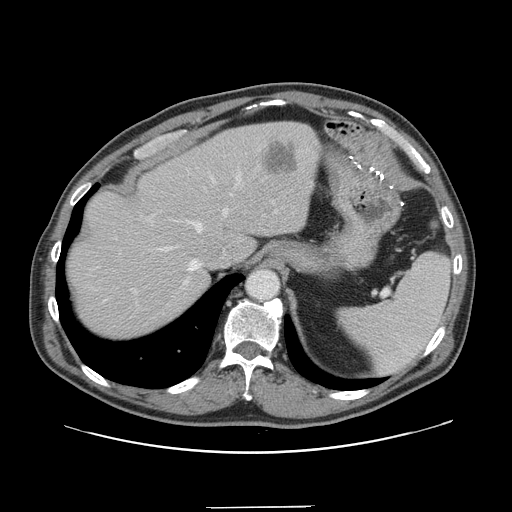
Contrast-enhanced abdominal CT, one axial slice. Position 115 of 139 along the scan axis. Intravenous contrast given. Soft-tissue window (W 400 / L 40 HU). 2.5 mm slice thickness. 512 × 512 image matrix, field of view 397 × 397 mm. Male patient, age 64 years. Case-level facts recorded for this patient, not image findings: diagnosis: colorectal cancer liver metastases, imaged before liver resection; multiple liver metastases: yes; largest metastasis: 3.5 cm; disease in both lobes: yes.
Annotated regions visible in this slice (expert manual segmentation):
- hepatic veins: bounding box (x1, y1, x2, y2) in pixels: (162, 174, 241, 284)
- liver: (66, 122, 320, 338)
- planned liver remnant (the part of the liver to remain after resection): (67, 125, 267, 338)
- portal vein (with intrahepatic branches): (133, 290, 137, 293)
- liver metastasis: (266, 139, 299, 175)